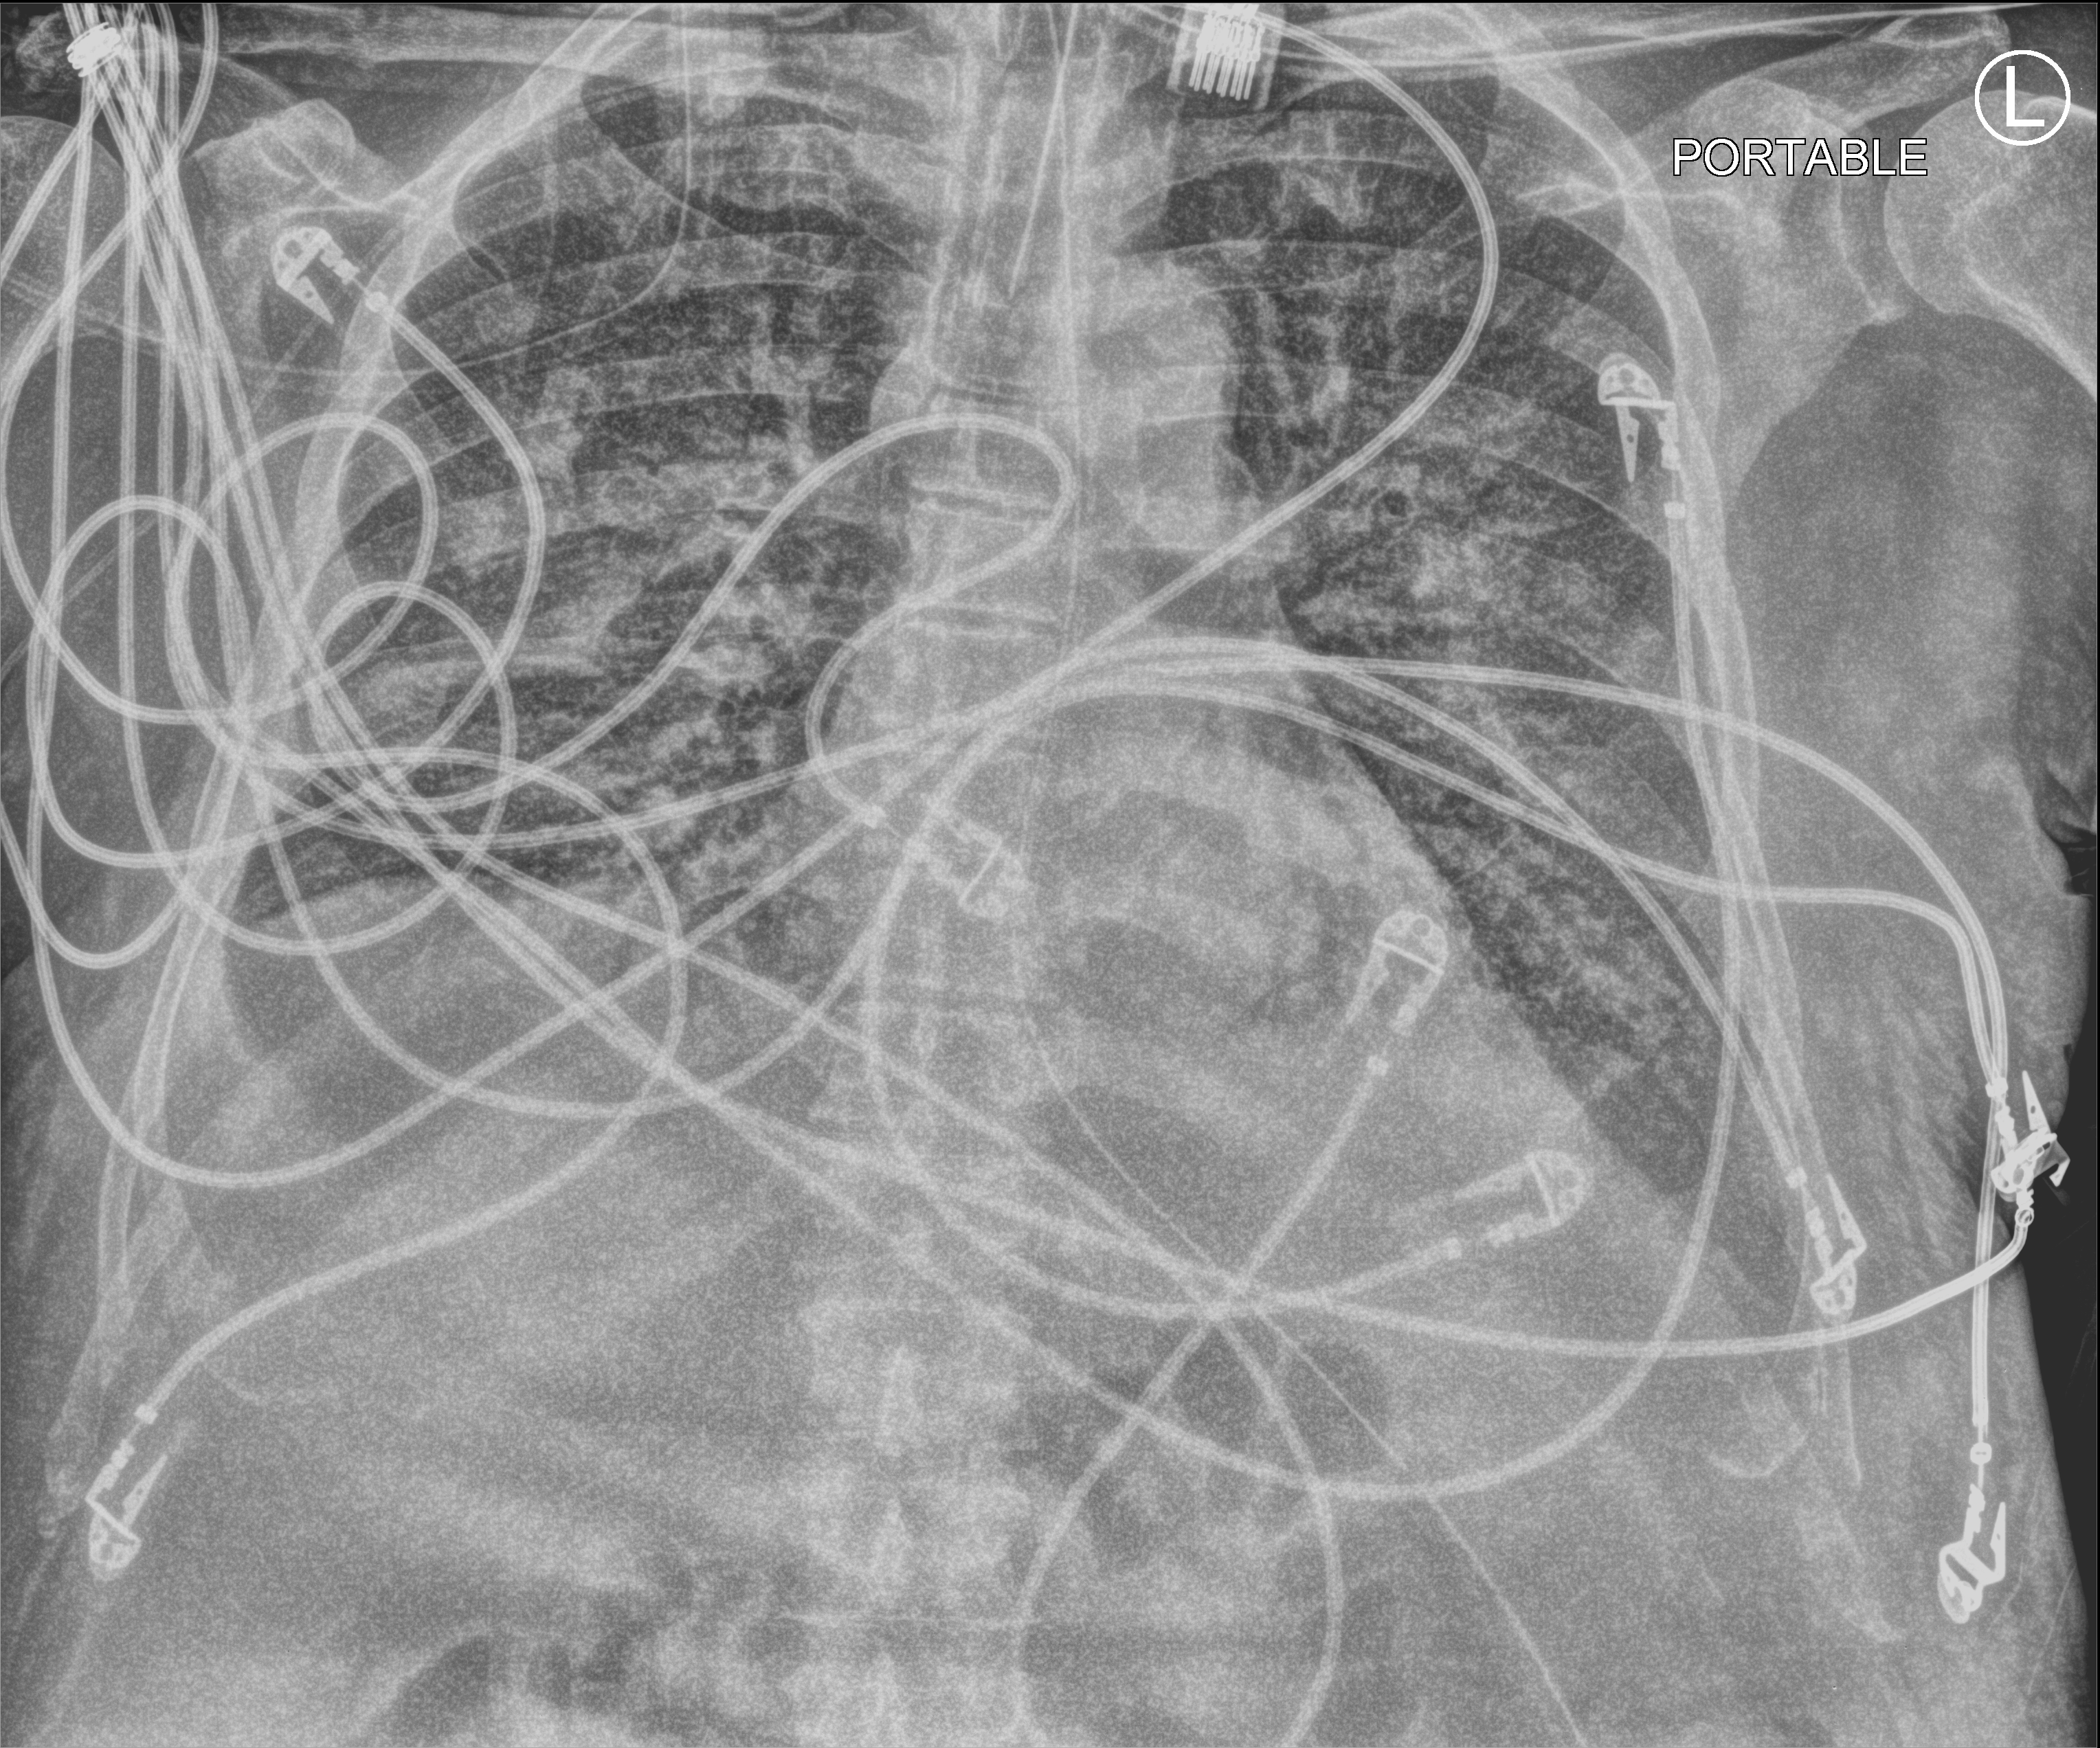
Chest X-ray (portable); anteroposterior (AP) projection. Patient hospitalised with COVID-19; male, aged 60–74 years.
Admission-level facts for this patient (not findings on this image; timing relative to this image not recorded): mechanically ventilated during this hospital stay: yes.